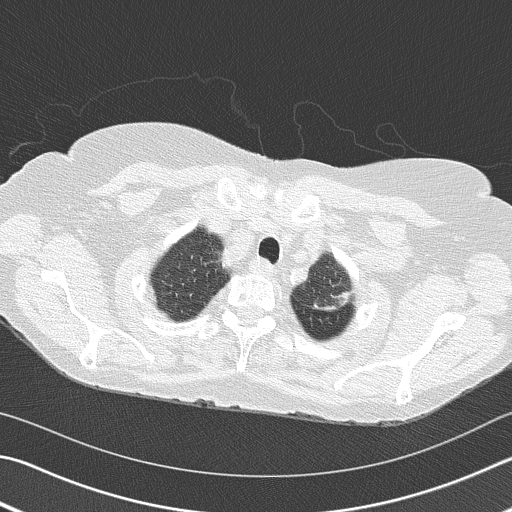
Axial slice from a low-dose chest CT screening exam. Second annual screen. Lung window (W 1500 / L -600 HU). 2 mm slice thickness. 120 kVp. 512 × 512 image matrix, field of view 342 × 342 mm. Female participant, aged 68 years at enrolment. Former smoker at enrolment.
Expert reader's lesion annotation, bounding box <288,252,366,333> (left, top, right, bottom; pixels). Screening reader's record for this exam (one nodule recorded; not confirmed to be the boxed lesion): non-calcified nodule or mass ≥4 mm, left upper lobe, 4 × 2 mm, spiculated (stellate) margins, soft tissue attenuation, pre-existing on the prior screen: yes; interval growth: yes. Official screen result: positive, other. Lung cancer was diagnosed 392 days after this screen: adenocarcinoma, NOS, left upper lobe, poorly differentiated (G3), stage IB (AJCC 6th edition), 50 mm at pathology.